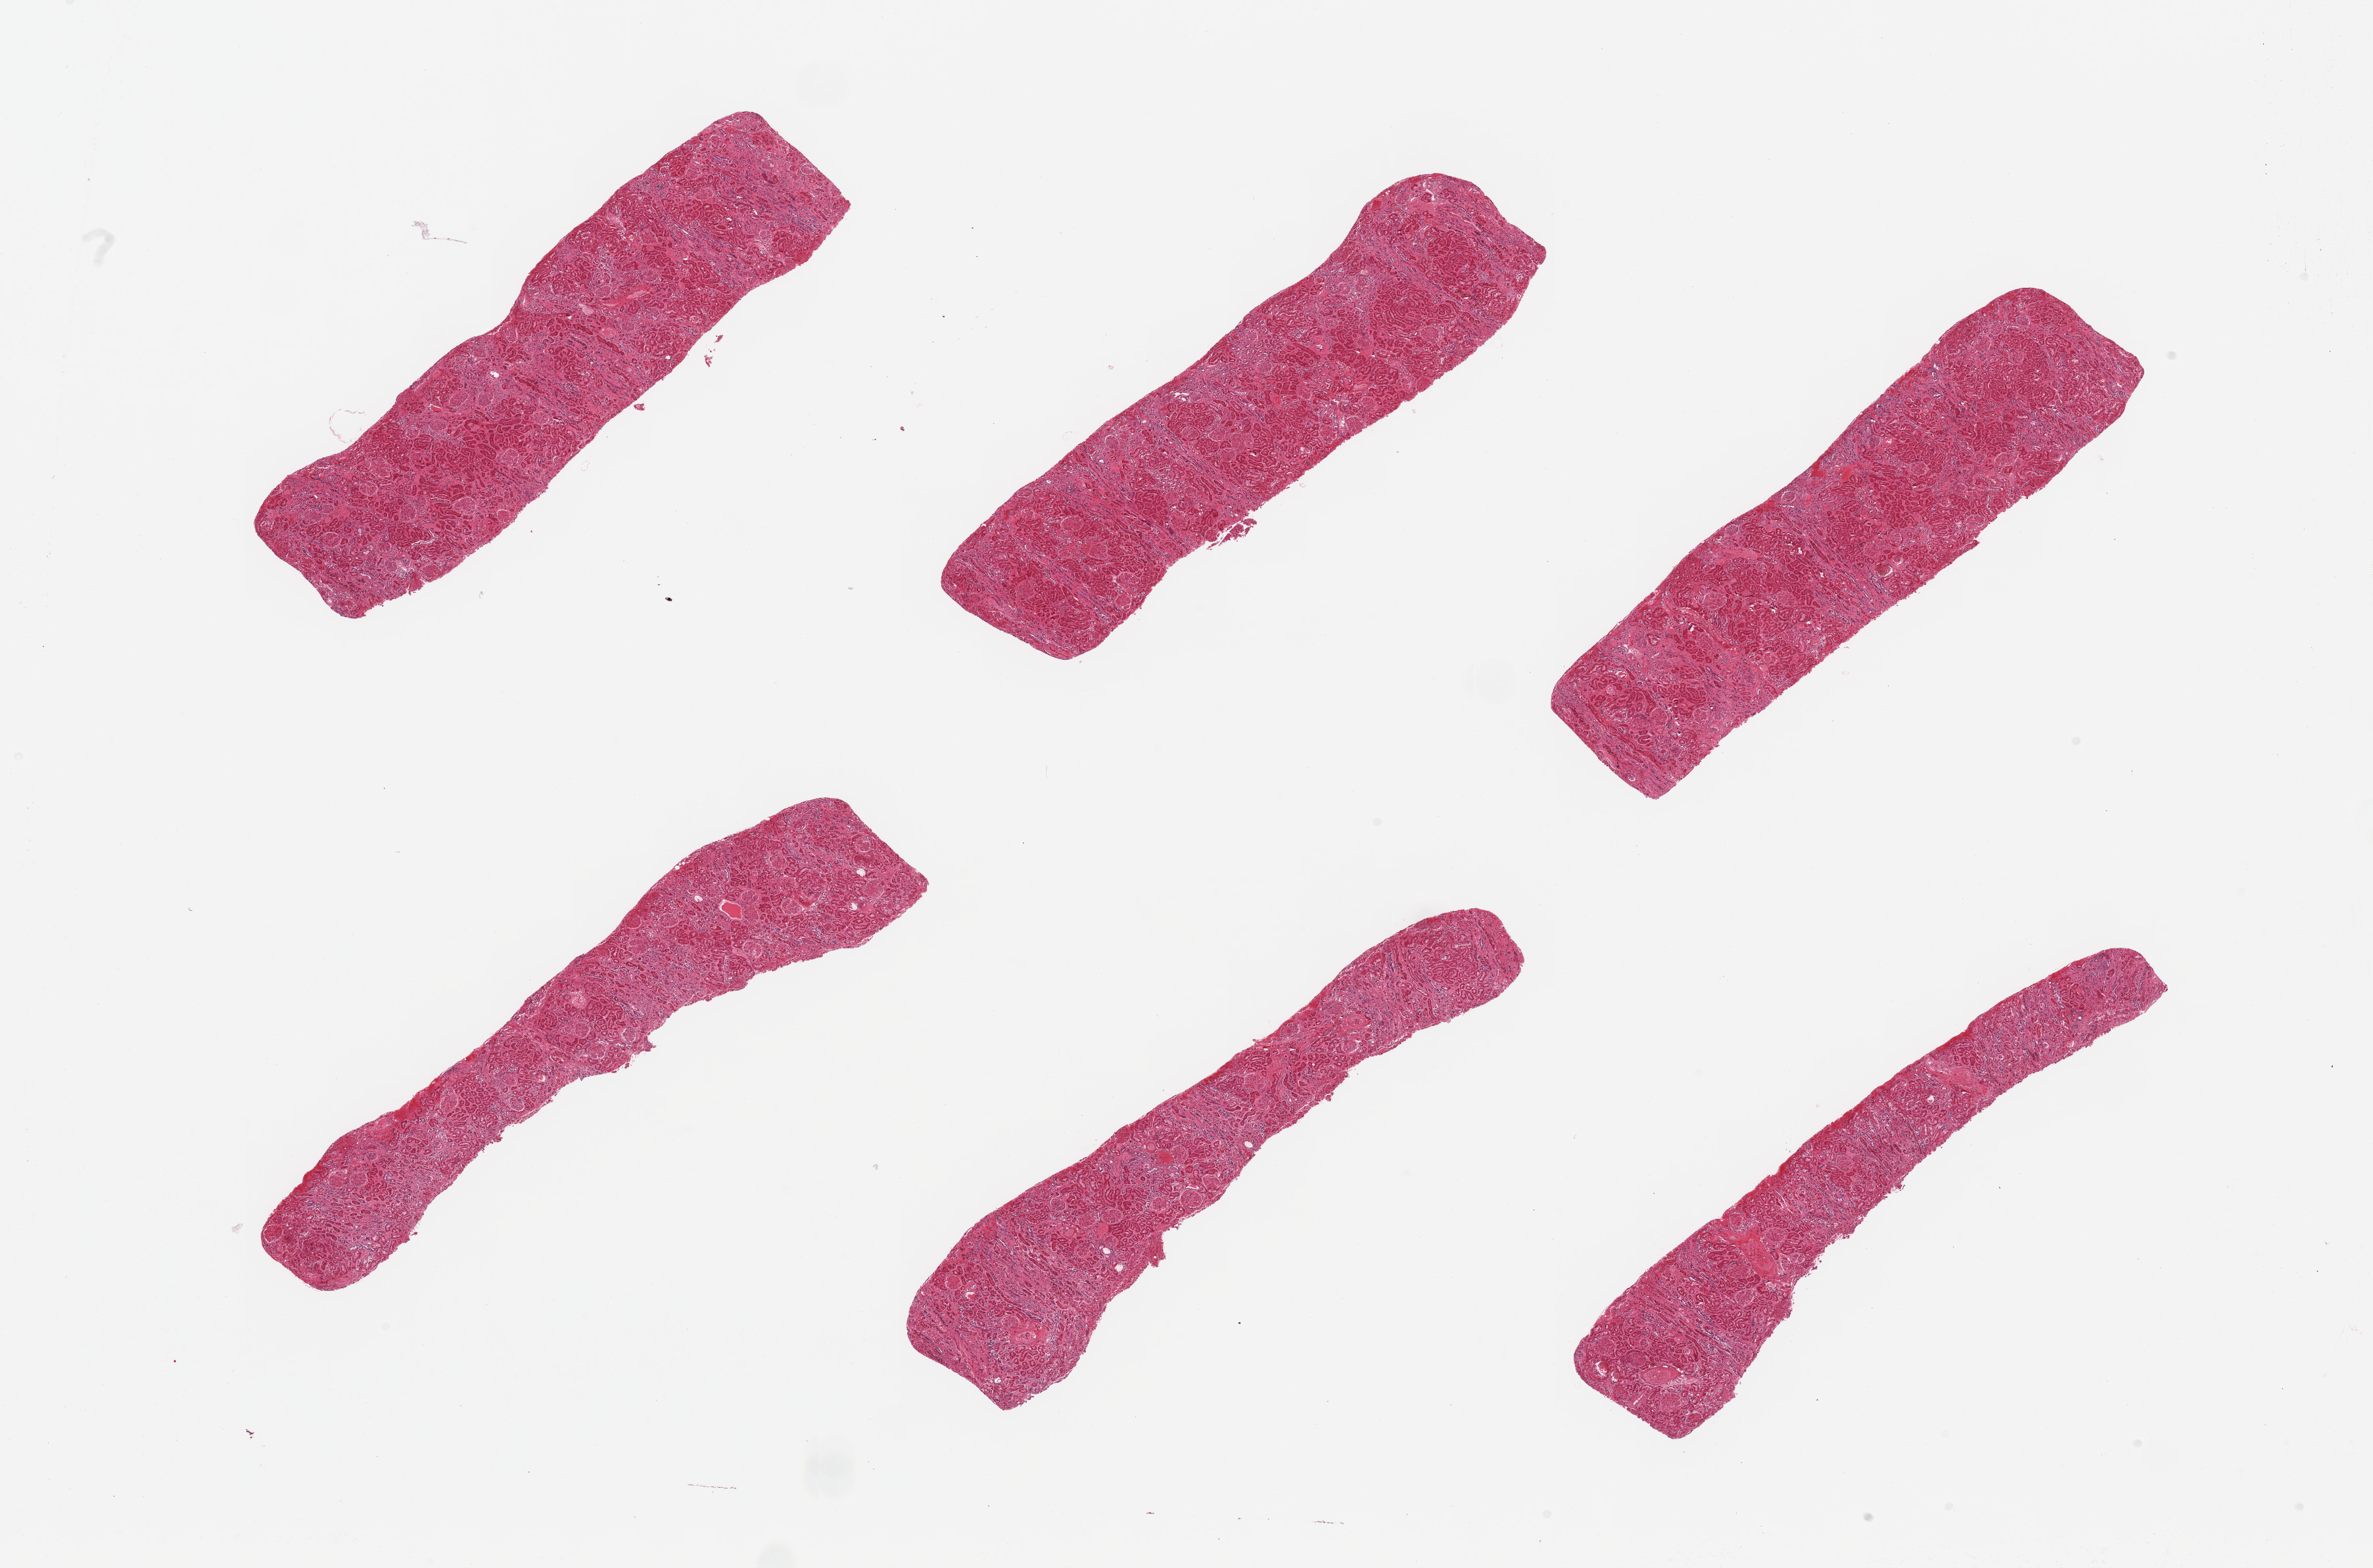
H&E whole-slide image, low-resolution overview of the scanned area, about 28.5 x 18.9 mm, PAXgene-fixed, paraffin-embedded tissue, sampled site (target tissue): renal cortex, tissue donor sample. Donor sex: male.
Review note (as recorded): 6 pieces; congestion, interstitial fibrosis, glomeruli in all sections.